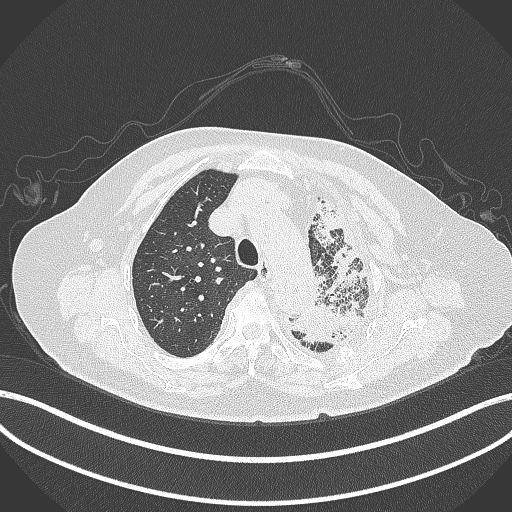
Chest CT, one axial slice. Slice 302 of 399 in the series (ordered by position). Lung window (W 1500 / L -600 HU). 512 × 512 image matrix. Patient: female, 75 years. From the clinical record (not read from this slice): clinical TNM (as recorded): T3 N3 M1.
Outlined on this slice (rectangle marked by the reading radiologist):
- lung tumour (recorded histology: adenocarcinoma): bounding box [x1, y1, x2, y2] px = [280, 297, 370, 351]